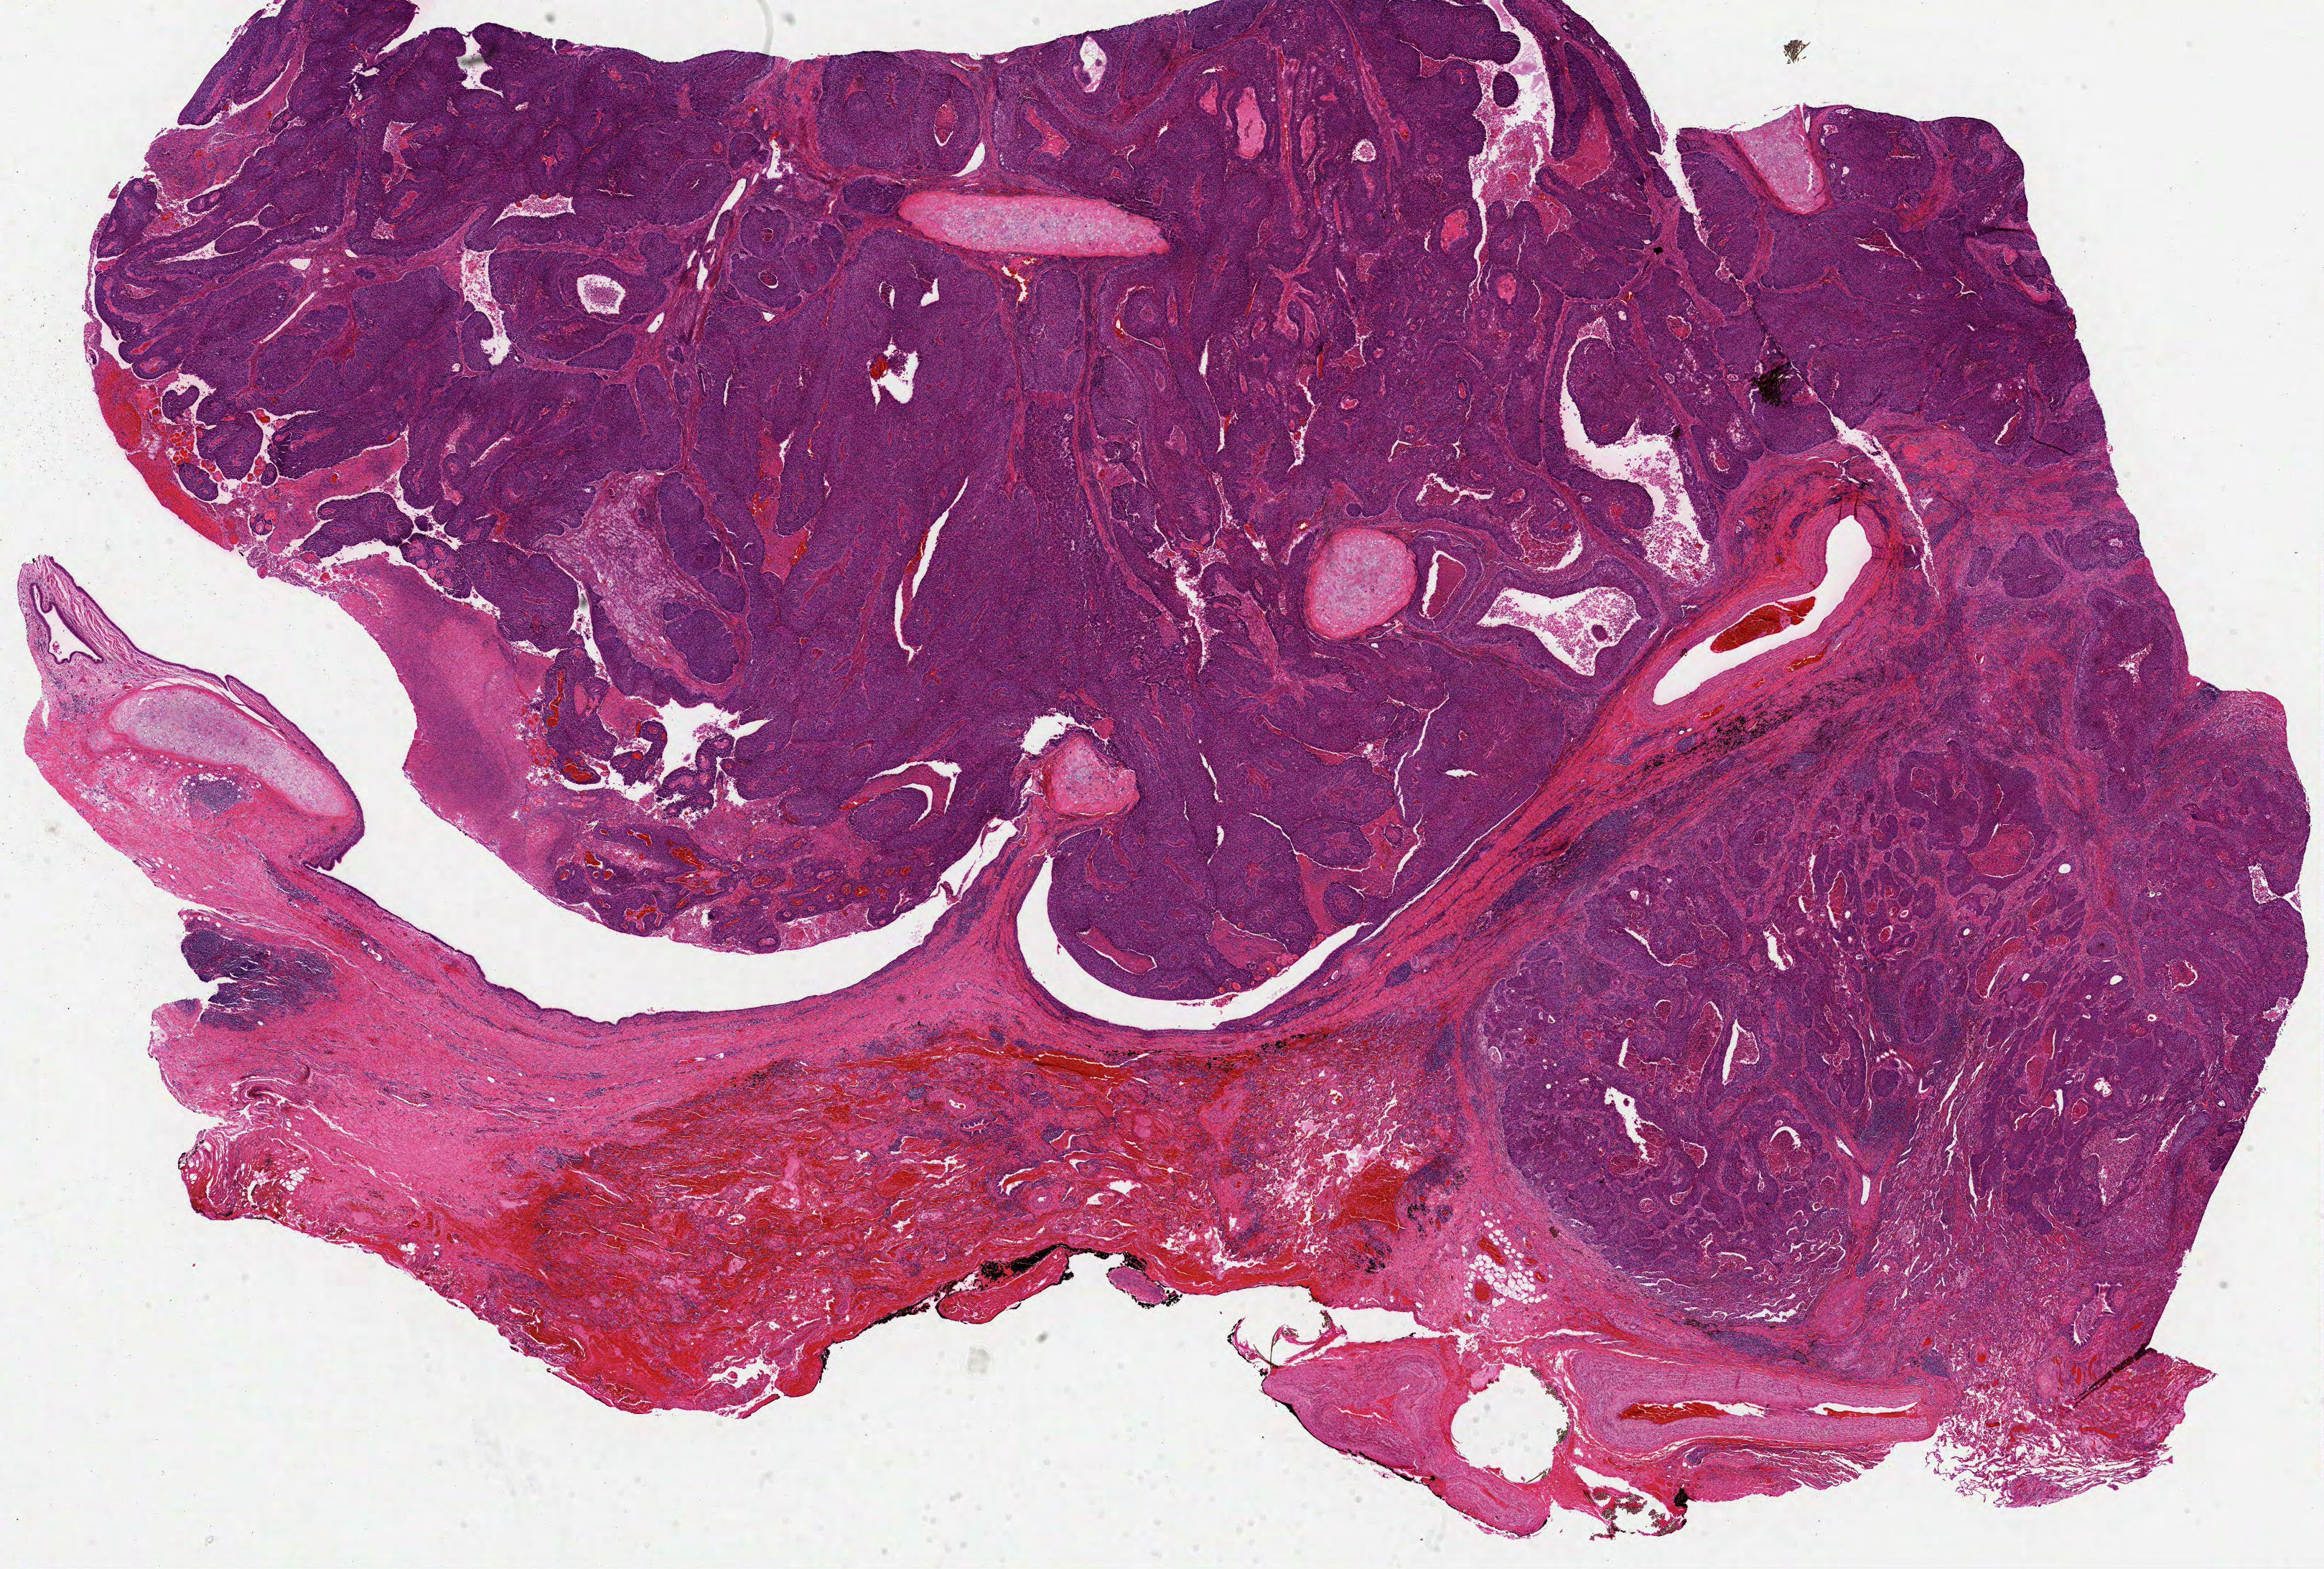
H&E whole-slide image, a low-resolution overview of the entire scanned area, about 26.1 x 17.6 mm (from a 40x scan), FFPE section, lung, primary tumour sample. Male, age 66 years at initial diagnosis.
Diagnosis: Squamous cell carcinoma, NOS. AJCC pathologic stage: IIIA (6th edition).